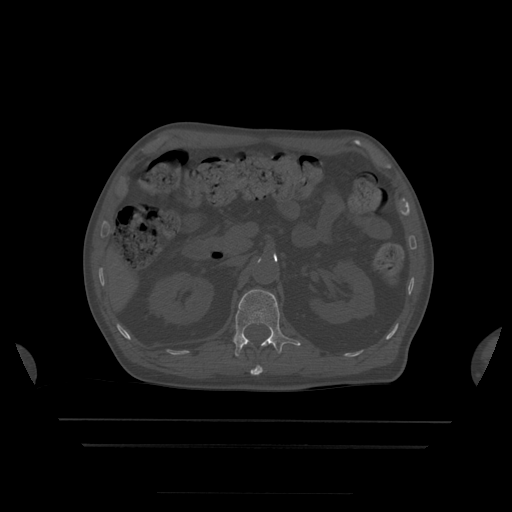
CT including the spine, one axial slice. Position 175 of 522 along the scan axis. Bone window (W 1800 / L 400 HU). 1.25 mm slice thickness. 512 × 512 image matrix, field of view 436 × 436 mm. Patient age 68 years. From the clinical record (not read from this slice): primary cancer: urothelial.
Structures marked on this image (semi-automatically segmented with operator editing):
- L1 vertebra: bounding box <233,289,301,357> (left, top, right, bottom; pixels)
- T12 vertebra: <251,366,263,376>